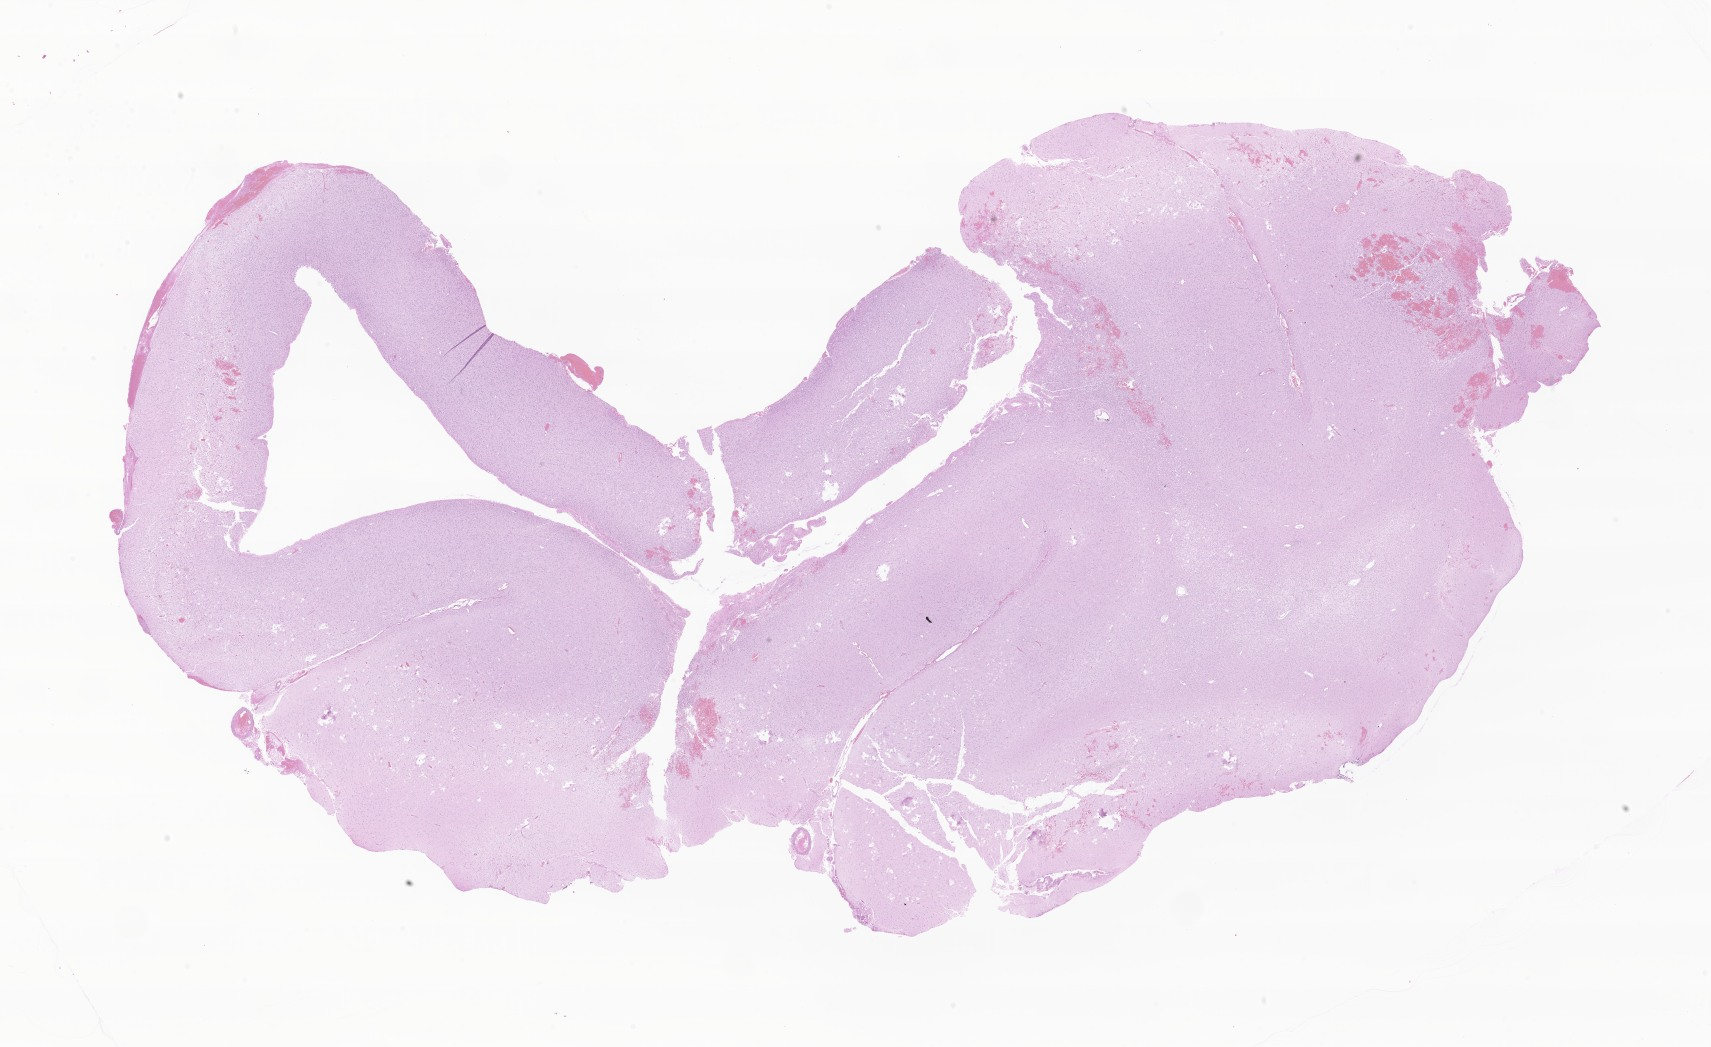
H&E whole-slide image of tumor tissue from the frontal lobe, low-resolution overview of the scanned area, about 28.9 x 17.7 mm, FFPE section. Patient male; age 41 months (3 years 5 months).
Diagnosis: Ganglioglioma, NOS.